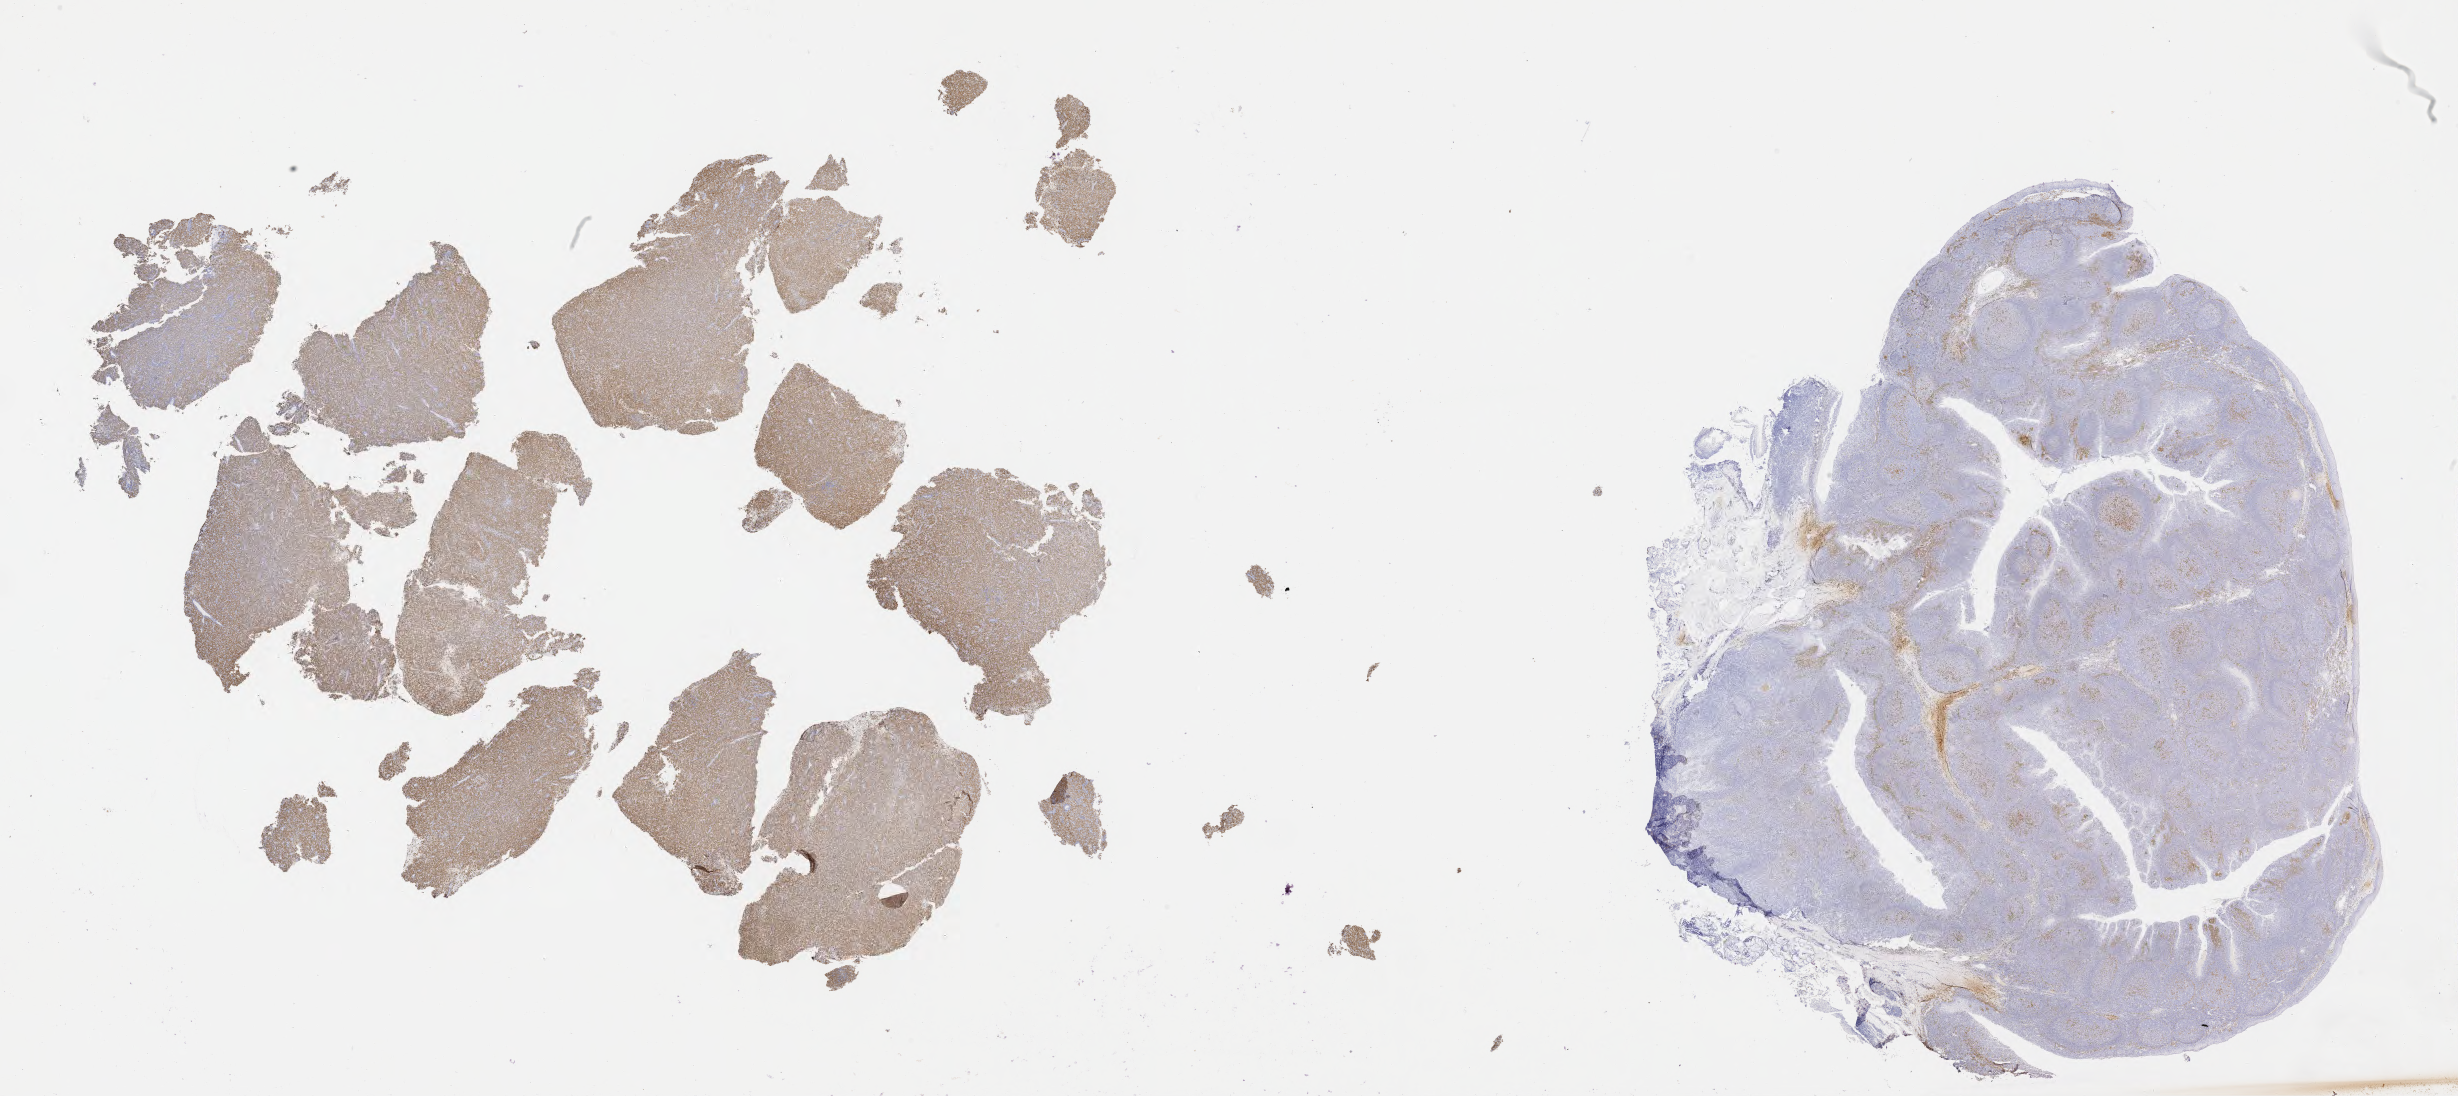
IHC for IRF4/MUM1, whole-slide image, low-resolution overview of the scanned area, about 39.7 x 17.7 mm. Specimen: tumor tissue. Anatomic site: lymph node. Patient: female, age 50 years.
Histologic diagnosis: Diffuse large B-cell lymphoma, NOS.